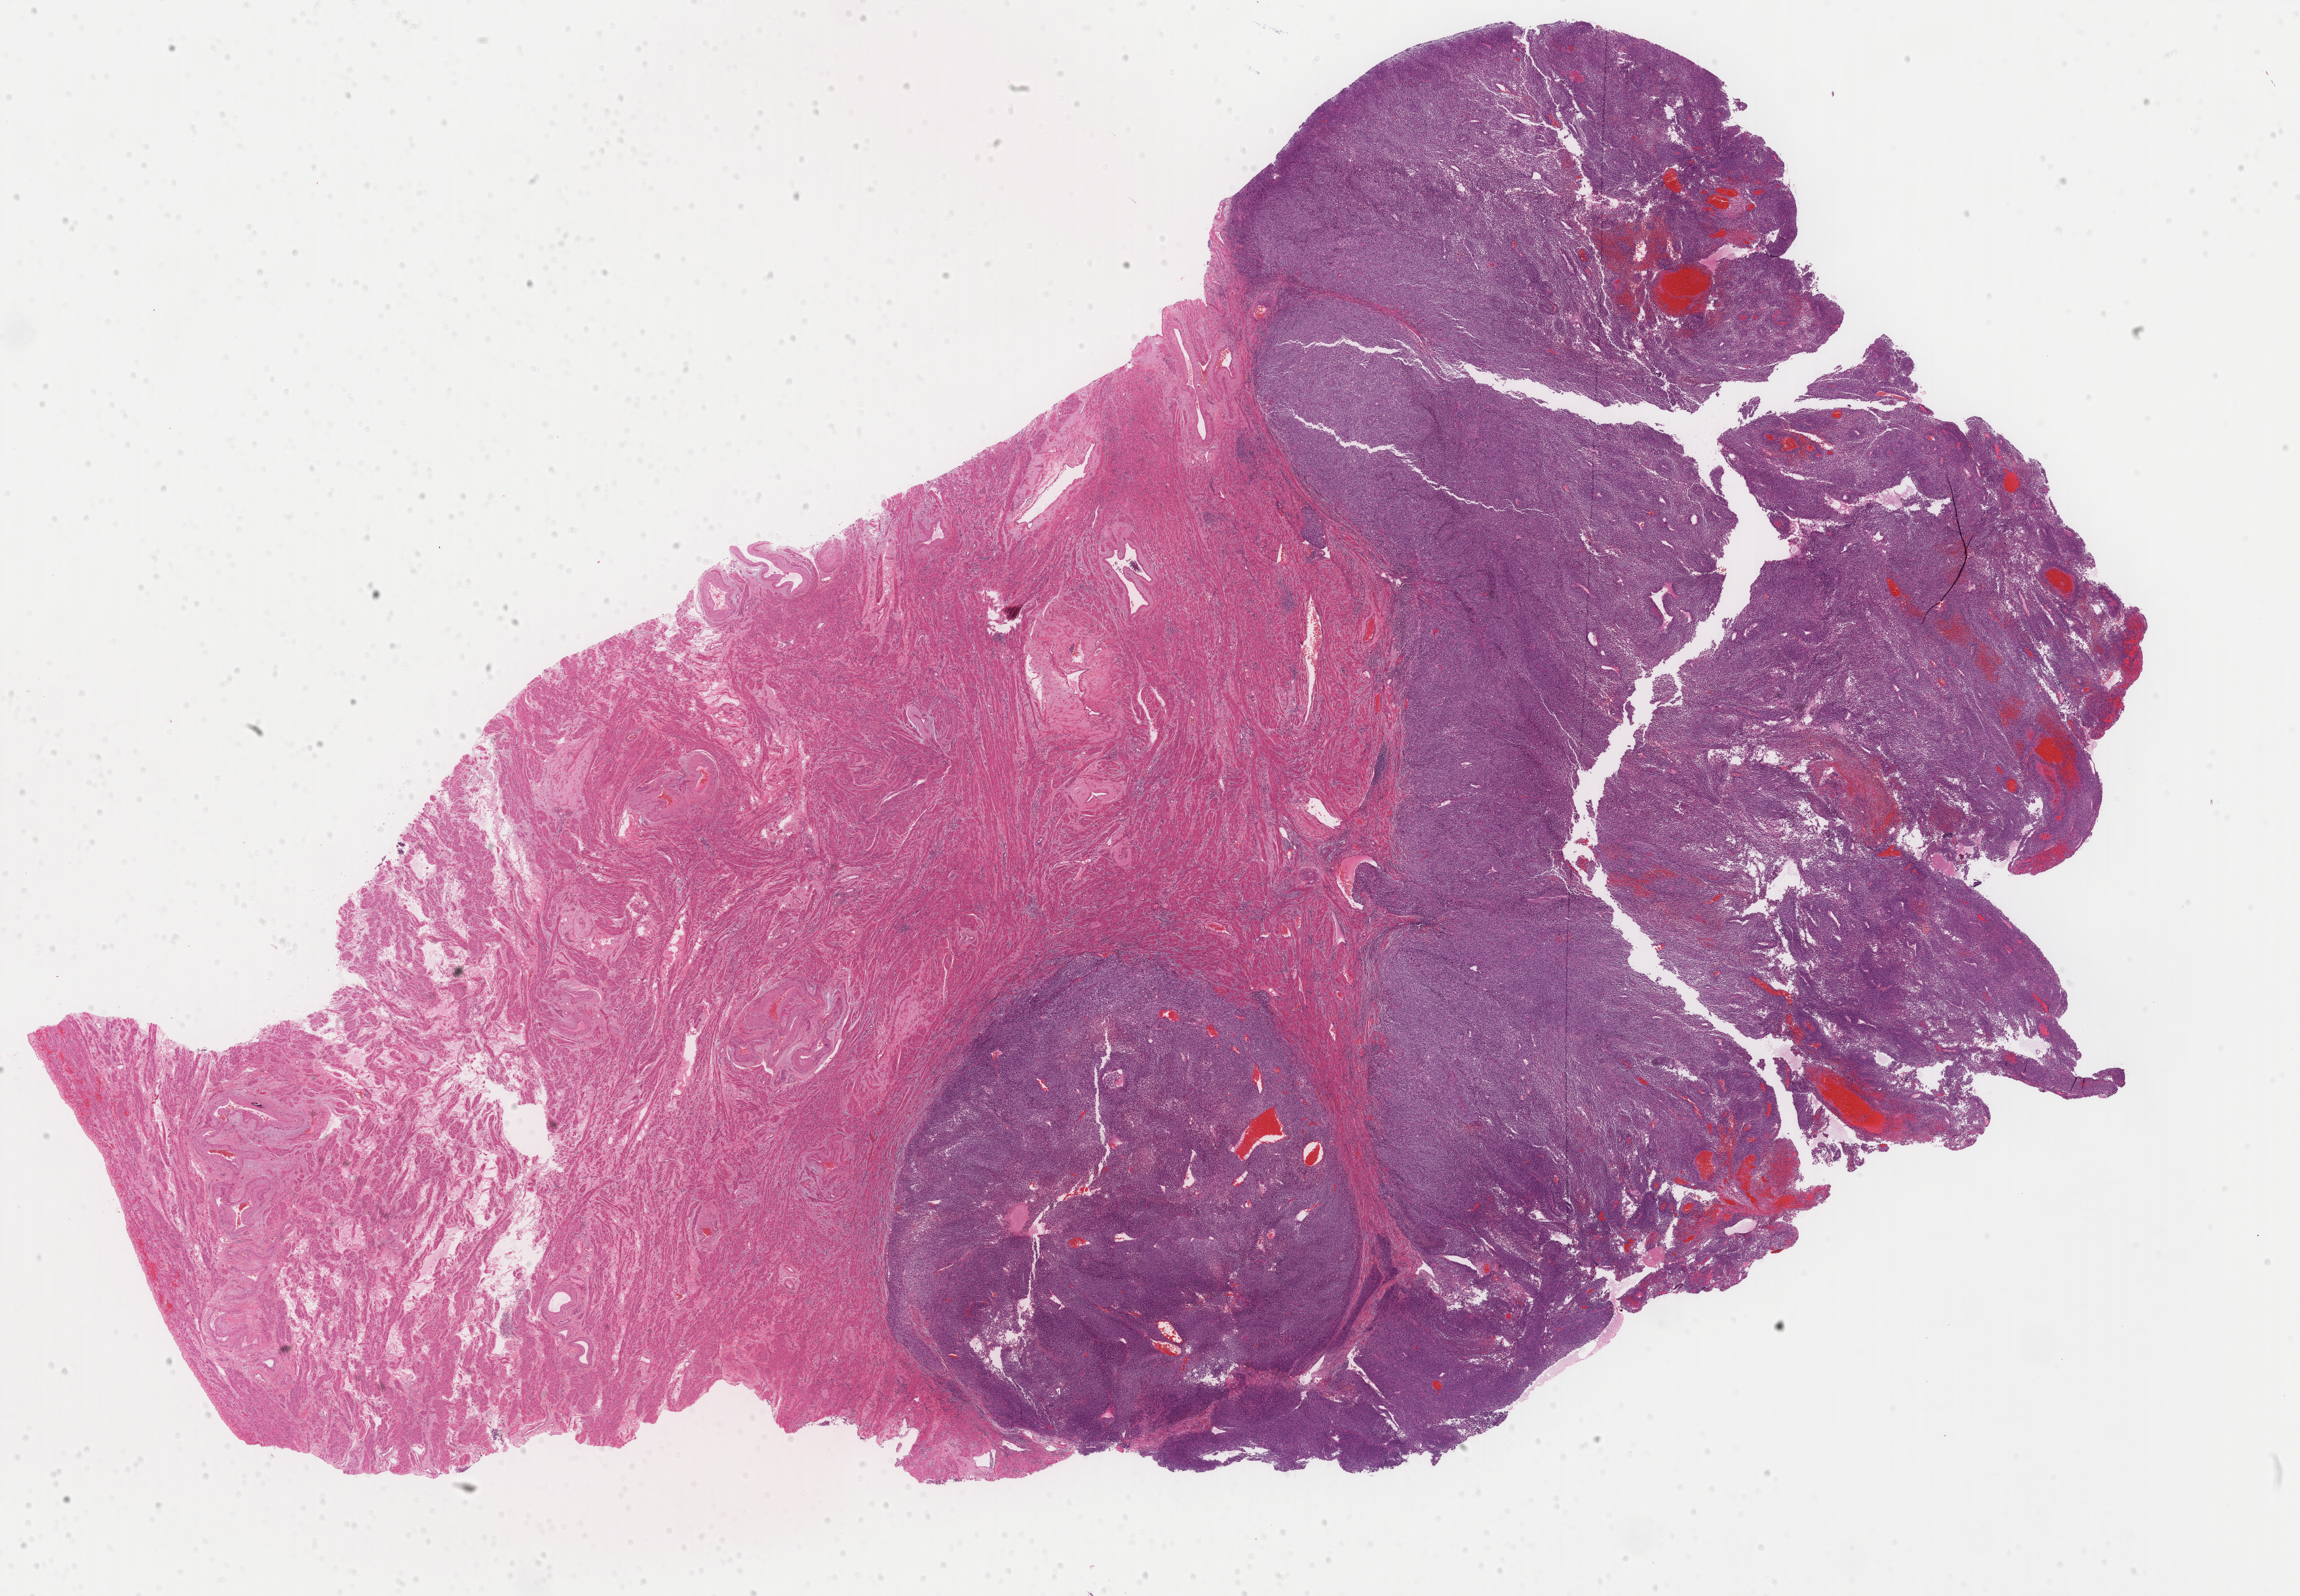
Whole-slide histology image, H&E-stained — shown as a low-resolution overview of the whole scanned area (about 27.9 x 19.3 mm, slide scanned at 40x). Formalin-fixed paraffin-embedded (FFPE) diagnostic section. Uterus, primary tumour sample. Female, age 83 years at initial diagnosis.
* histologic diagnosis: Mullerian mixed tumor (fundus uteri)
* lymph nodes positive (case pathology): 0 of 12 examined
* FIGO stage: IB